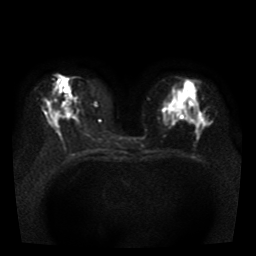
Breast MRI, one axial slice; position 13 of 38 along the scan axis; diffusion-weighted series; image 2 of 4 stored at this slice position (different b-values; order by instance number); 1.5 T; 5 mm slice thickness; 256 × 256 image matrix, field of view 330 × 330 mm. Female patient.
Structures marked on this image (manually delineated by an expert):
- tumour on diffusion-weighted imaging: bounding box [x1, y1, x2, y2] px = [201, 118, 211, 126]